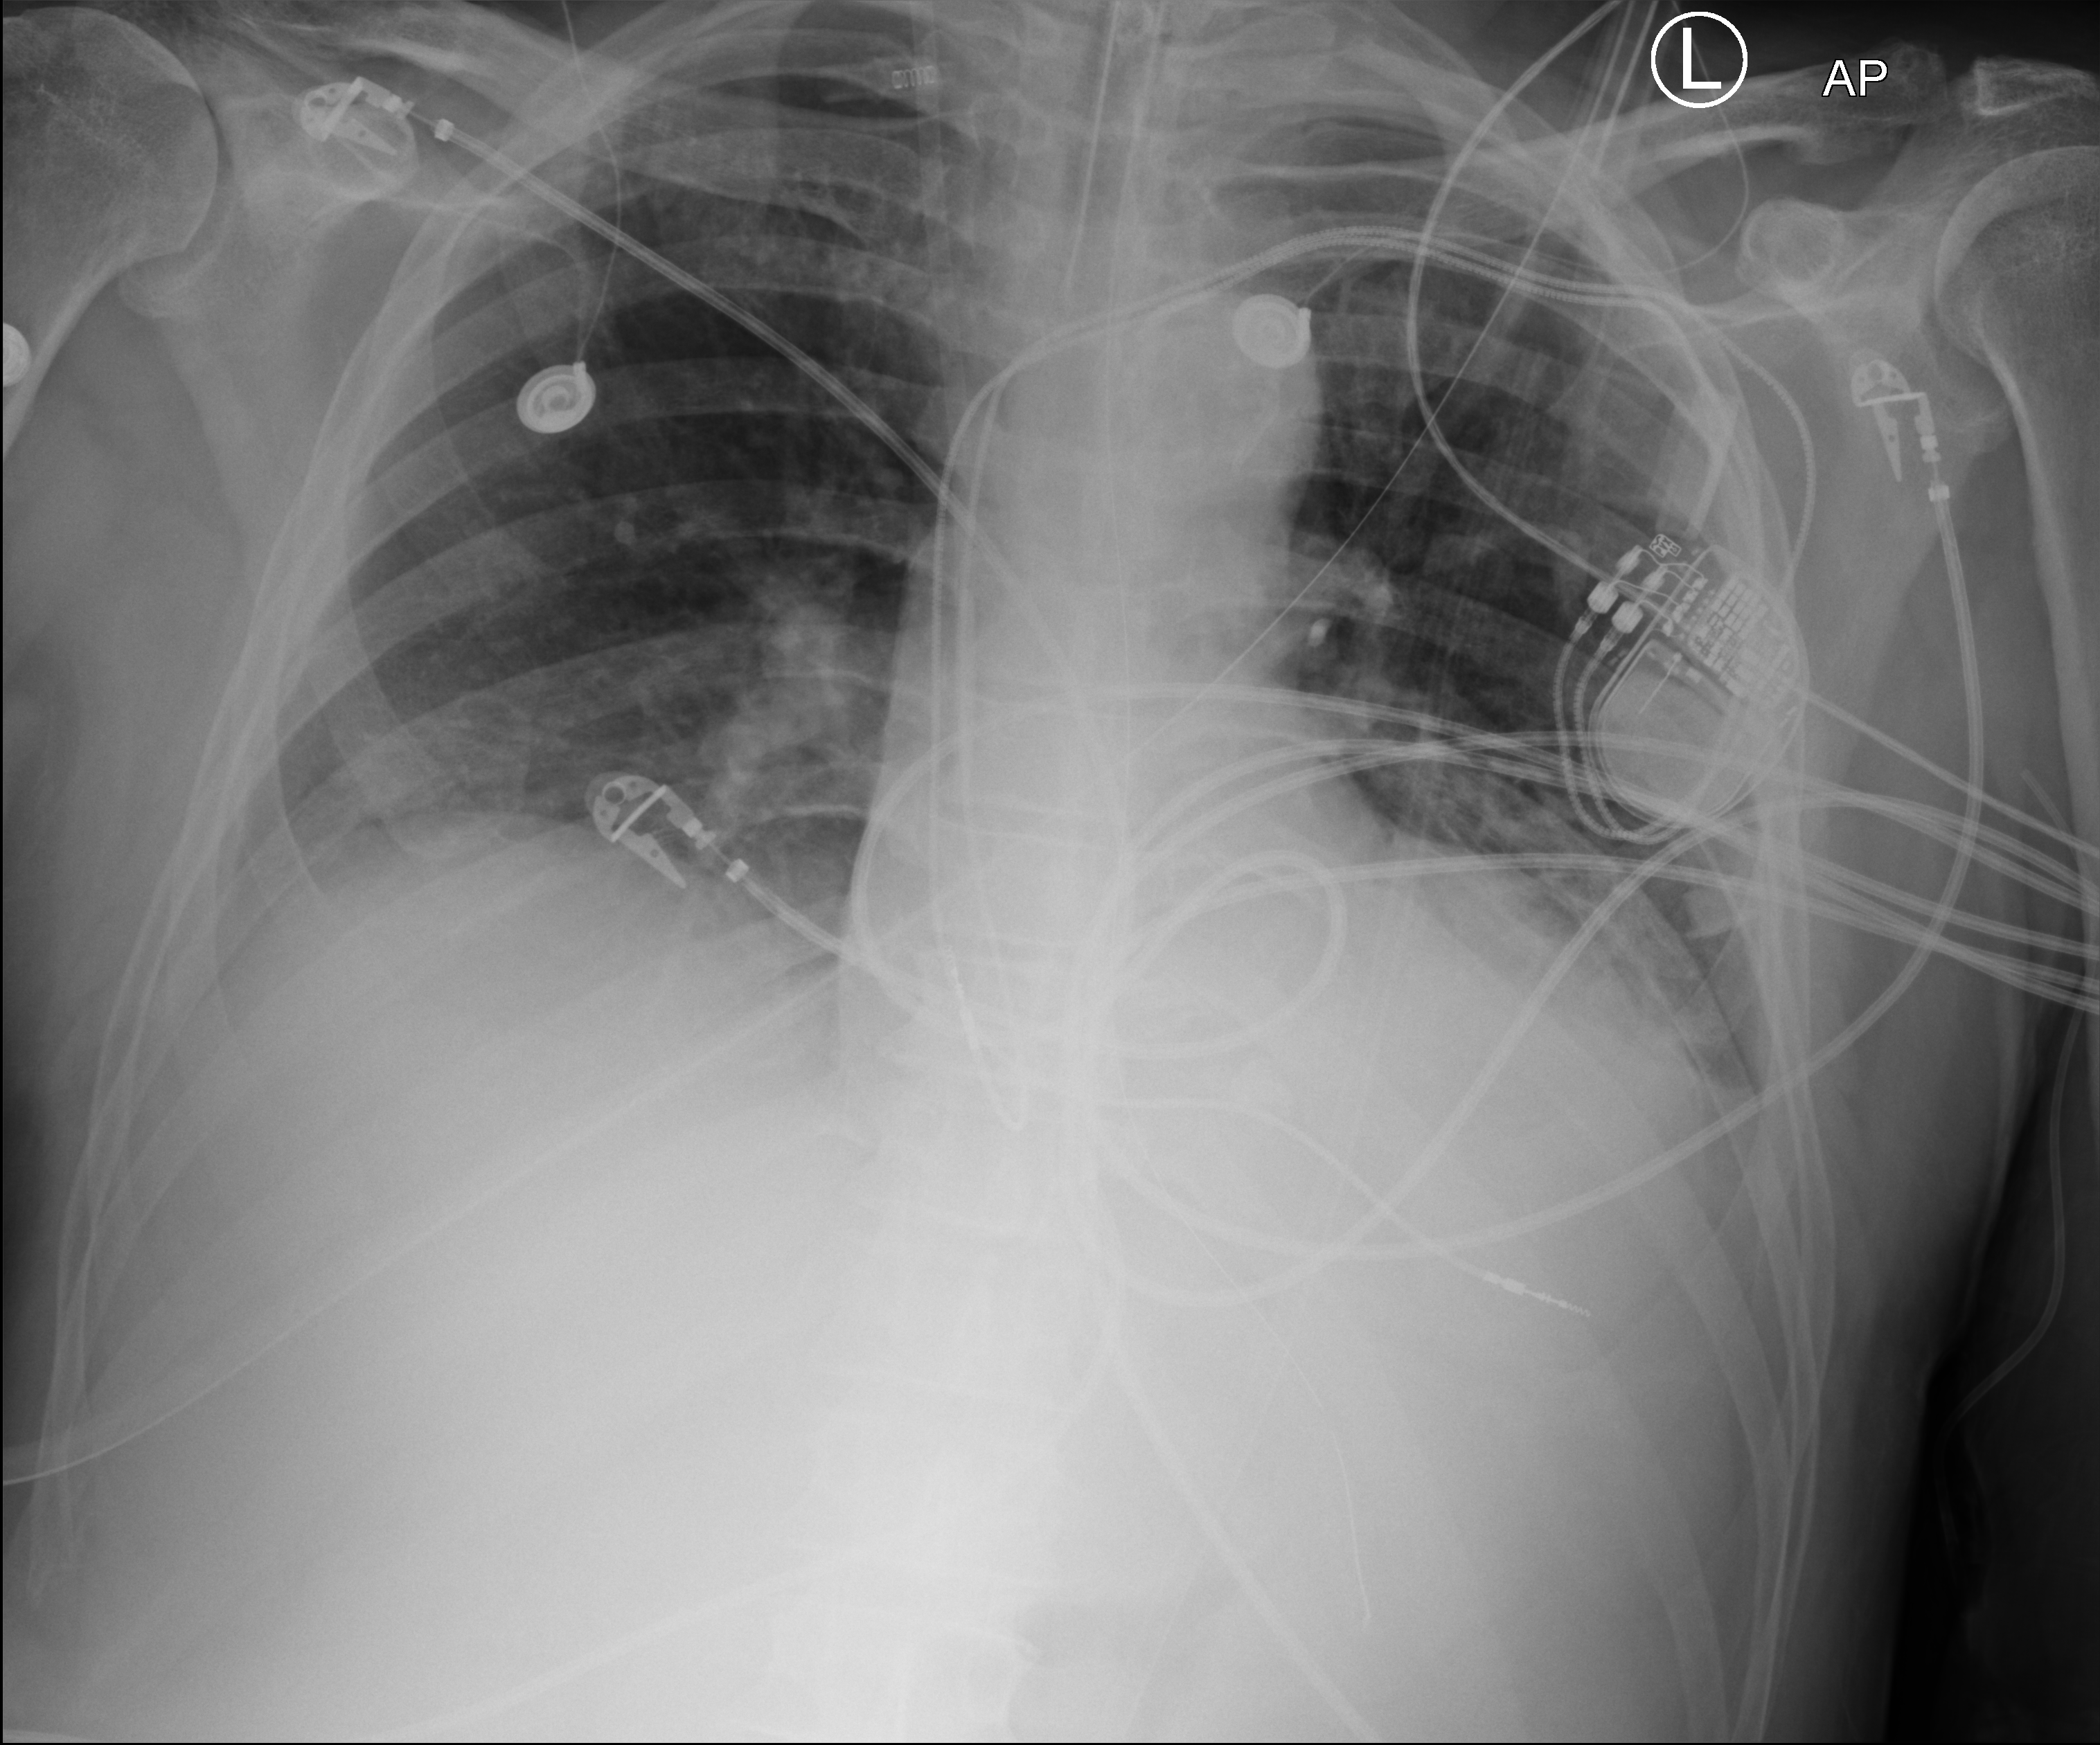
Chest X-ray (portable), anteroposterior (AP) projection. Male patient hospitalised with COVID-19, age 60–74 years.
From the hospital-stay record, not from the radiograph (when in the stay this image was taken is not recorded): admitted to intensive care during this hospital stay: yes.